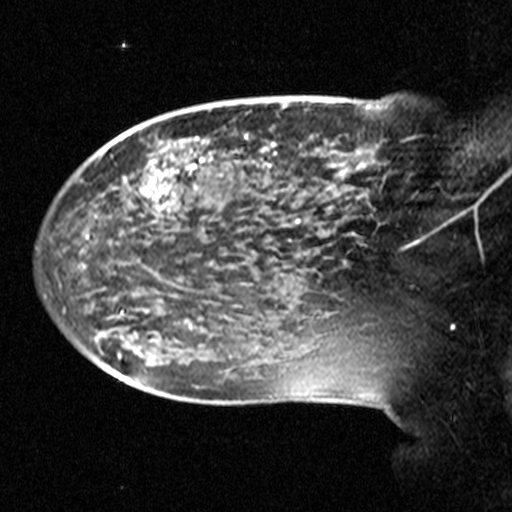
Breast MRI (dynamic contrast-enhanced), one sagittal slice; slice 12 of 44 in the series (ordered by position); dynamic contrast-enhanced study with each time point stored as its own series, time point 2 of 3 at this slice position (early post-contrast, ordered by acquisition time); 1.5 T; TE 4.5 ms, TR 11 ms; 3 mm slice thickness; 512 × 512 image matrix, field of view 240 × 240 mm. Female patient, age 38 years. Case-level facts recorded for this patient, not image findings: setting: breast cancer imaged before/during neoadjuvant chemotherapy; receptor status: HR-positive, HER2-negative.
Annotated regions visible in this slice (semi-automatically segmented with operator editing):
- analysis volume of interest (the breast-tissue region the enhancement analysis was run in; not a lesion): bounding box <124,106,405,245> (left, top, right, bottom; pixels)
- tumour enhancement mask (voxels above the 90 % enhancement threshold inside the analysis volume of interest): <147,152,277,194>